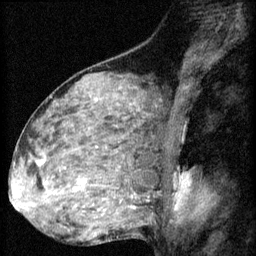
Breast MRI (dynamic contrast-enhanced), one sagittal slice; slice 36 of 60 in the series (ordered by position); 3 images stored at this slice position (order not interpretable as contrast timing); 1.5 T; TE 4.2 ms, TR 8.2 ms; 2 mm slice thickness; 256 × 256 image matrix, field of view 180 × 180 mm. Patient: female, 48 years.
Outlined on this slice (semi-automatically segmented with operator editing):
- analysis volume of interest (the breast-tissue region the enhancement analysis was run in; not a lesion): bounding box [x1, y1, x2, y2] px = [48, 160, 125, 217]
- tumour enhancement mask (voxels above the 70 % enhancement threshold inside the analysis volume of interest): [77, 180, 86, 191]